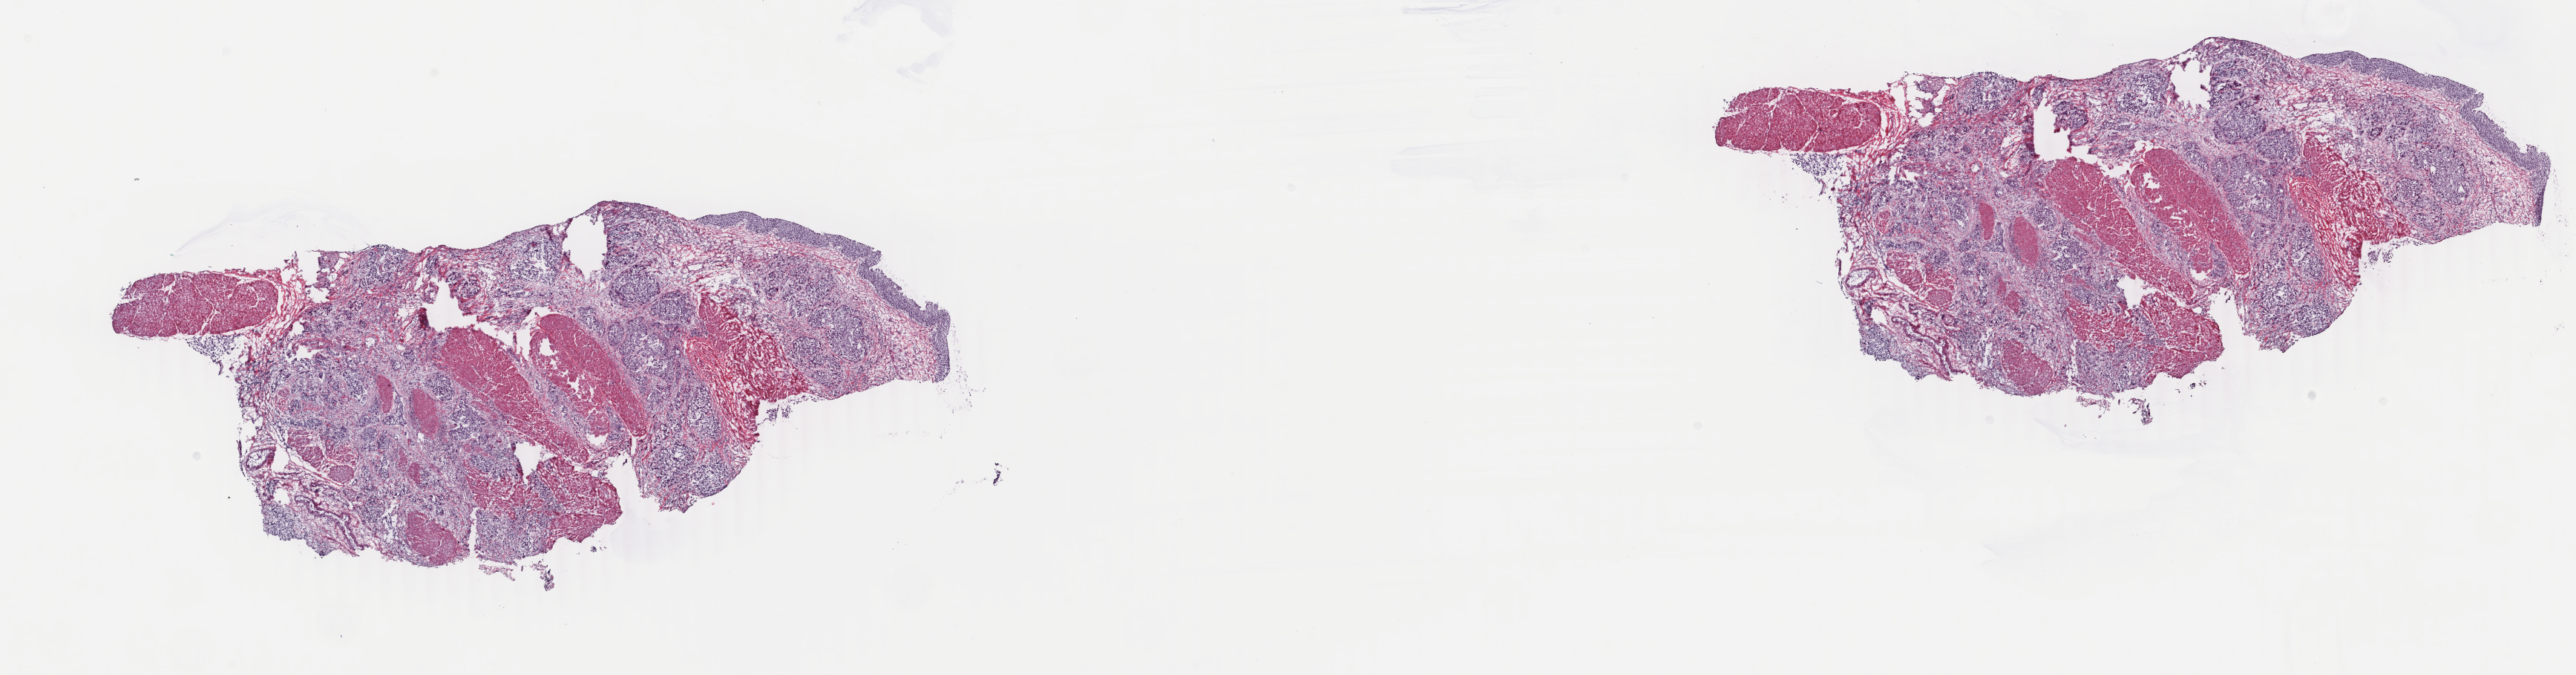
Digitized Hematoxylin and eosin (H&E) stained tissue section (whole slide) — shown as a low-resolution overview of the whole scanned area (about 27.6 x 7.2 mm). Frozen section from the top of the tissue portion. Sample: primary tumour, bladder. Patient: male, age at initial diagnosis 70 years. Histologic grade: high grade. Composition of this section per pathologist review: tumour cells 38%, tumour nuclei 75%, normal cells 4%, stromal cells 56%, necrosis 2%. Infiltration values recorded for this section: lymphocyte infiltration 4%, monocyte infiltration 1%, neutrophil infiltration 1%.
• lymph nodes positive (case pathology): 0 of 7 examined
• TNM: T3a N0 M0
• histologic diagnosis: Transitional cell carcinoma (lateral wall of bladder)
• AJCC pathologic stage: III (7th edition)